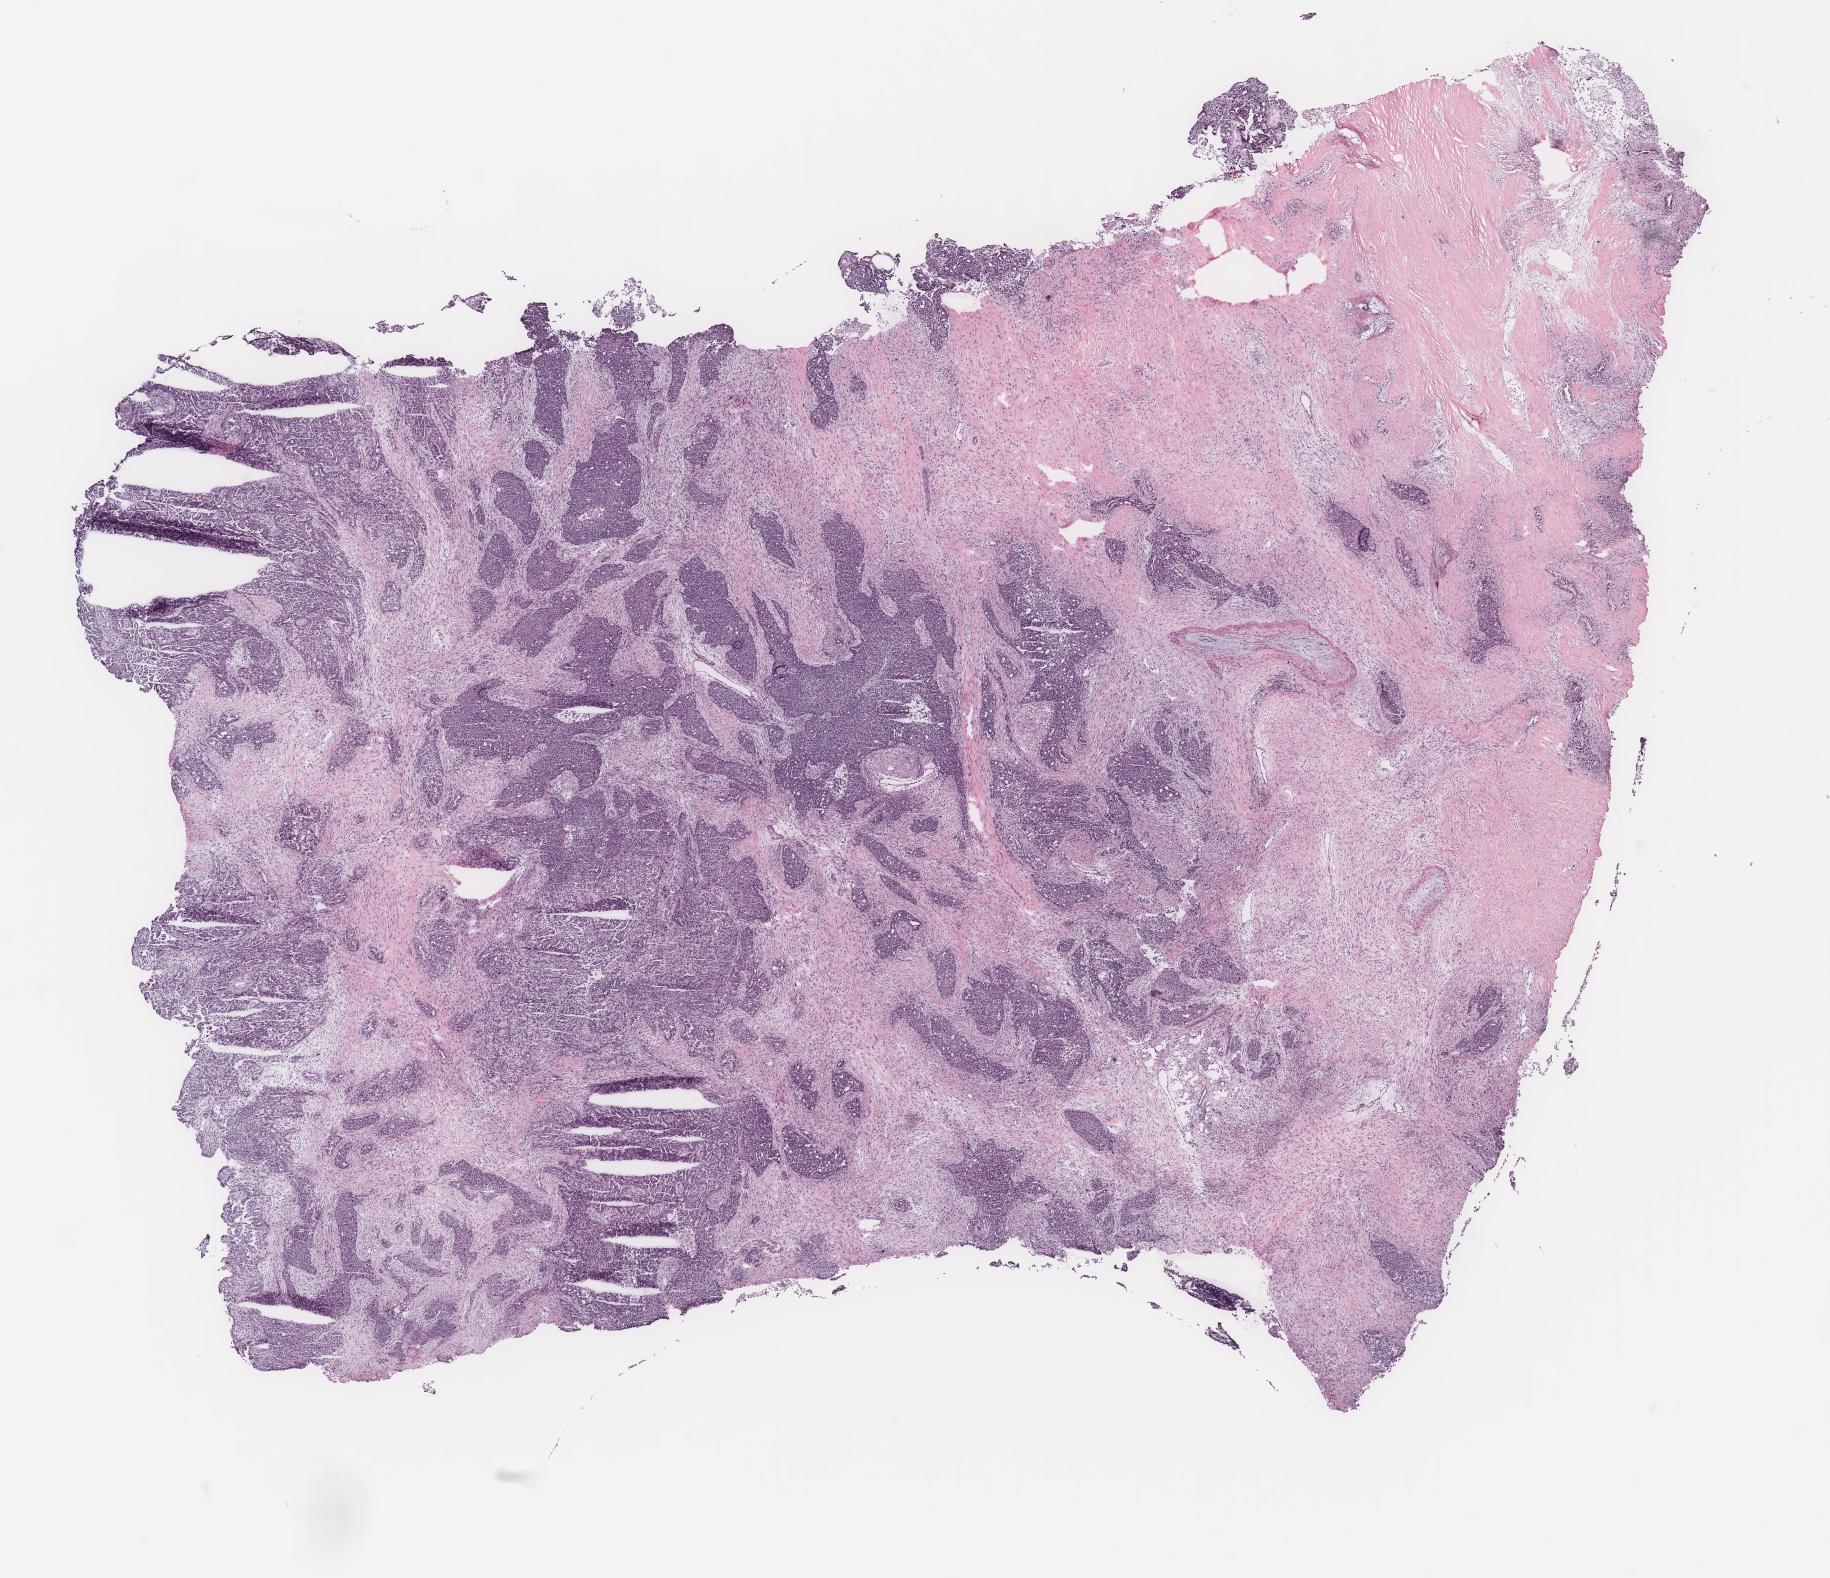
Digitized Hematoxylin and eosin (H&E) stained tissue section (whole slide), whole scanned area (about 14.6 x 12.6 mm) shown as a low-resolution overview, ovary, tissue type not recorded. Patient sex: female.
Patient diagnosis: Serous adenocarcinoma, NOS.